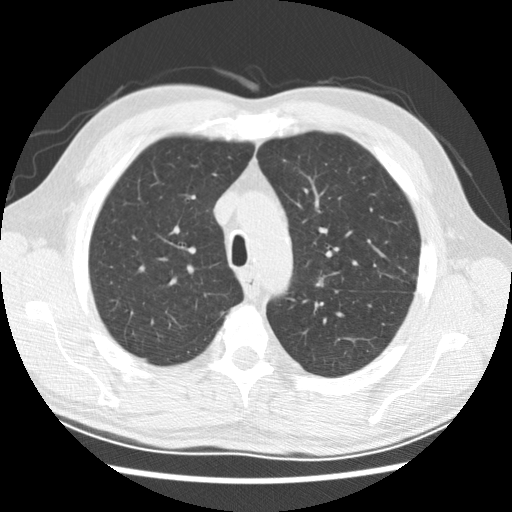
Low-dose screening chest CT, axial slice, baseline screening round, lung window (W 1500 / L -600 HU), 2.5 mm slice thickness, standard (soft-tissue) reconstruction kernel (STANDARD), 512 × 512 image matrix. Male participant, aged 59 years at enrolment. Current smoker at enrolment.
Expert-annotated lung lesion, box from (x=303, y=267) to (x=341, y=296) px. Reader record for this screening exam (exam-level; its link to the box is not recorded): non-calcified nodule or mass ≥4 mm, left upper lobe, 8 × 5 mm, smooth margins, soft tissue attenuation. Later outcome: lung cancer diagnosed 645 days after this screen (after the second annual screen) — adenocarcinoma, NOS, left upper lobe, left lower lobe, poorly differentiated (G3), stage IV (AJCC 6th edition).